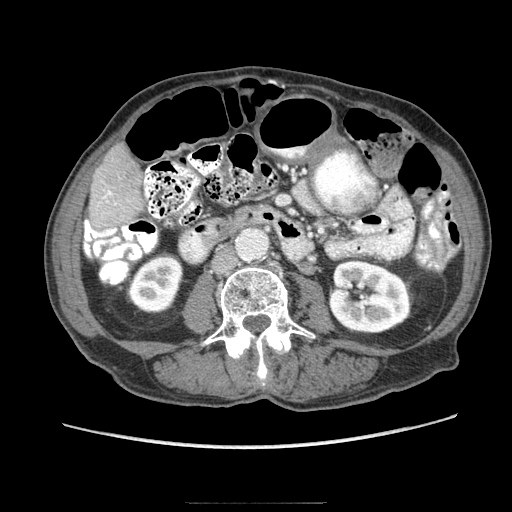
Contrast-enhanced abdominal CT (liver protocol), one axial slice; position 17 of 83 along the scan axis; soft-tissue window (W 400 / L 40 HU); 512 × 512 image matrix, field of view 360 × 360 mm. From the clinical record (not read from this slice): diagnosis: hepatocellular carcinoma (patient treated with transarterial chemoembolisation; whether this scan precedes or follows treatment is not stated here); TNM stage (as recorded): Stage-I; Child-Pugh class: A.
Annotated regions visible in this slice (semi-automatic segmentation, software-assisted and operator-edited):
- liver parenchyma outside the tumour (the mass and vessels are separate outlines, so this box may not span the whole liver): bounding box (x1, y1, x2, y2) in pixels: (84, 144, 144, 247)
- liver vessels: (84, 191, 116, 246)